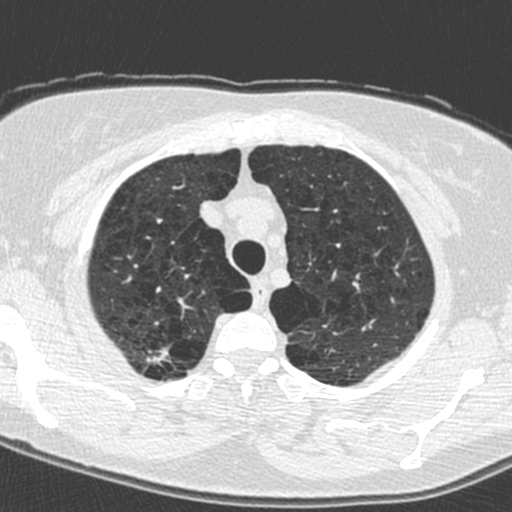
Low-dose screening chest CT, axial slice, baseline annual screen, lung window (W 1500 / L -600 HU), 1.3 mm slice thickness, standard (soft-tissue) reconstruction kernel (C), 120 kVp, 512 × 512 image matrix, field of view 278 × 278 mm. Female participant, aged 59 years at enrolment. Current smoker at enrolment.
Lesion marked by an expert reader, bounding box <132,336,177,375> (left, top, right, bottom; pixels). No non-calcified nodule or mass ≥4 mm was recorded by the screening reader at this exam. Lung cancer was diagnosed 881 days after this screen (after the third annual screen): adenocarcinoma, NOS, right upper lobe, poorly differentiated (G3), stage IA (AJCC 6th edition), 20 mm at pathology.